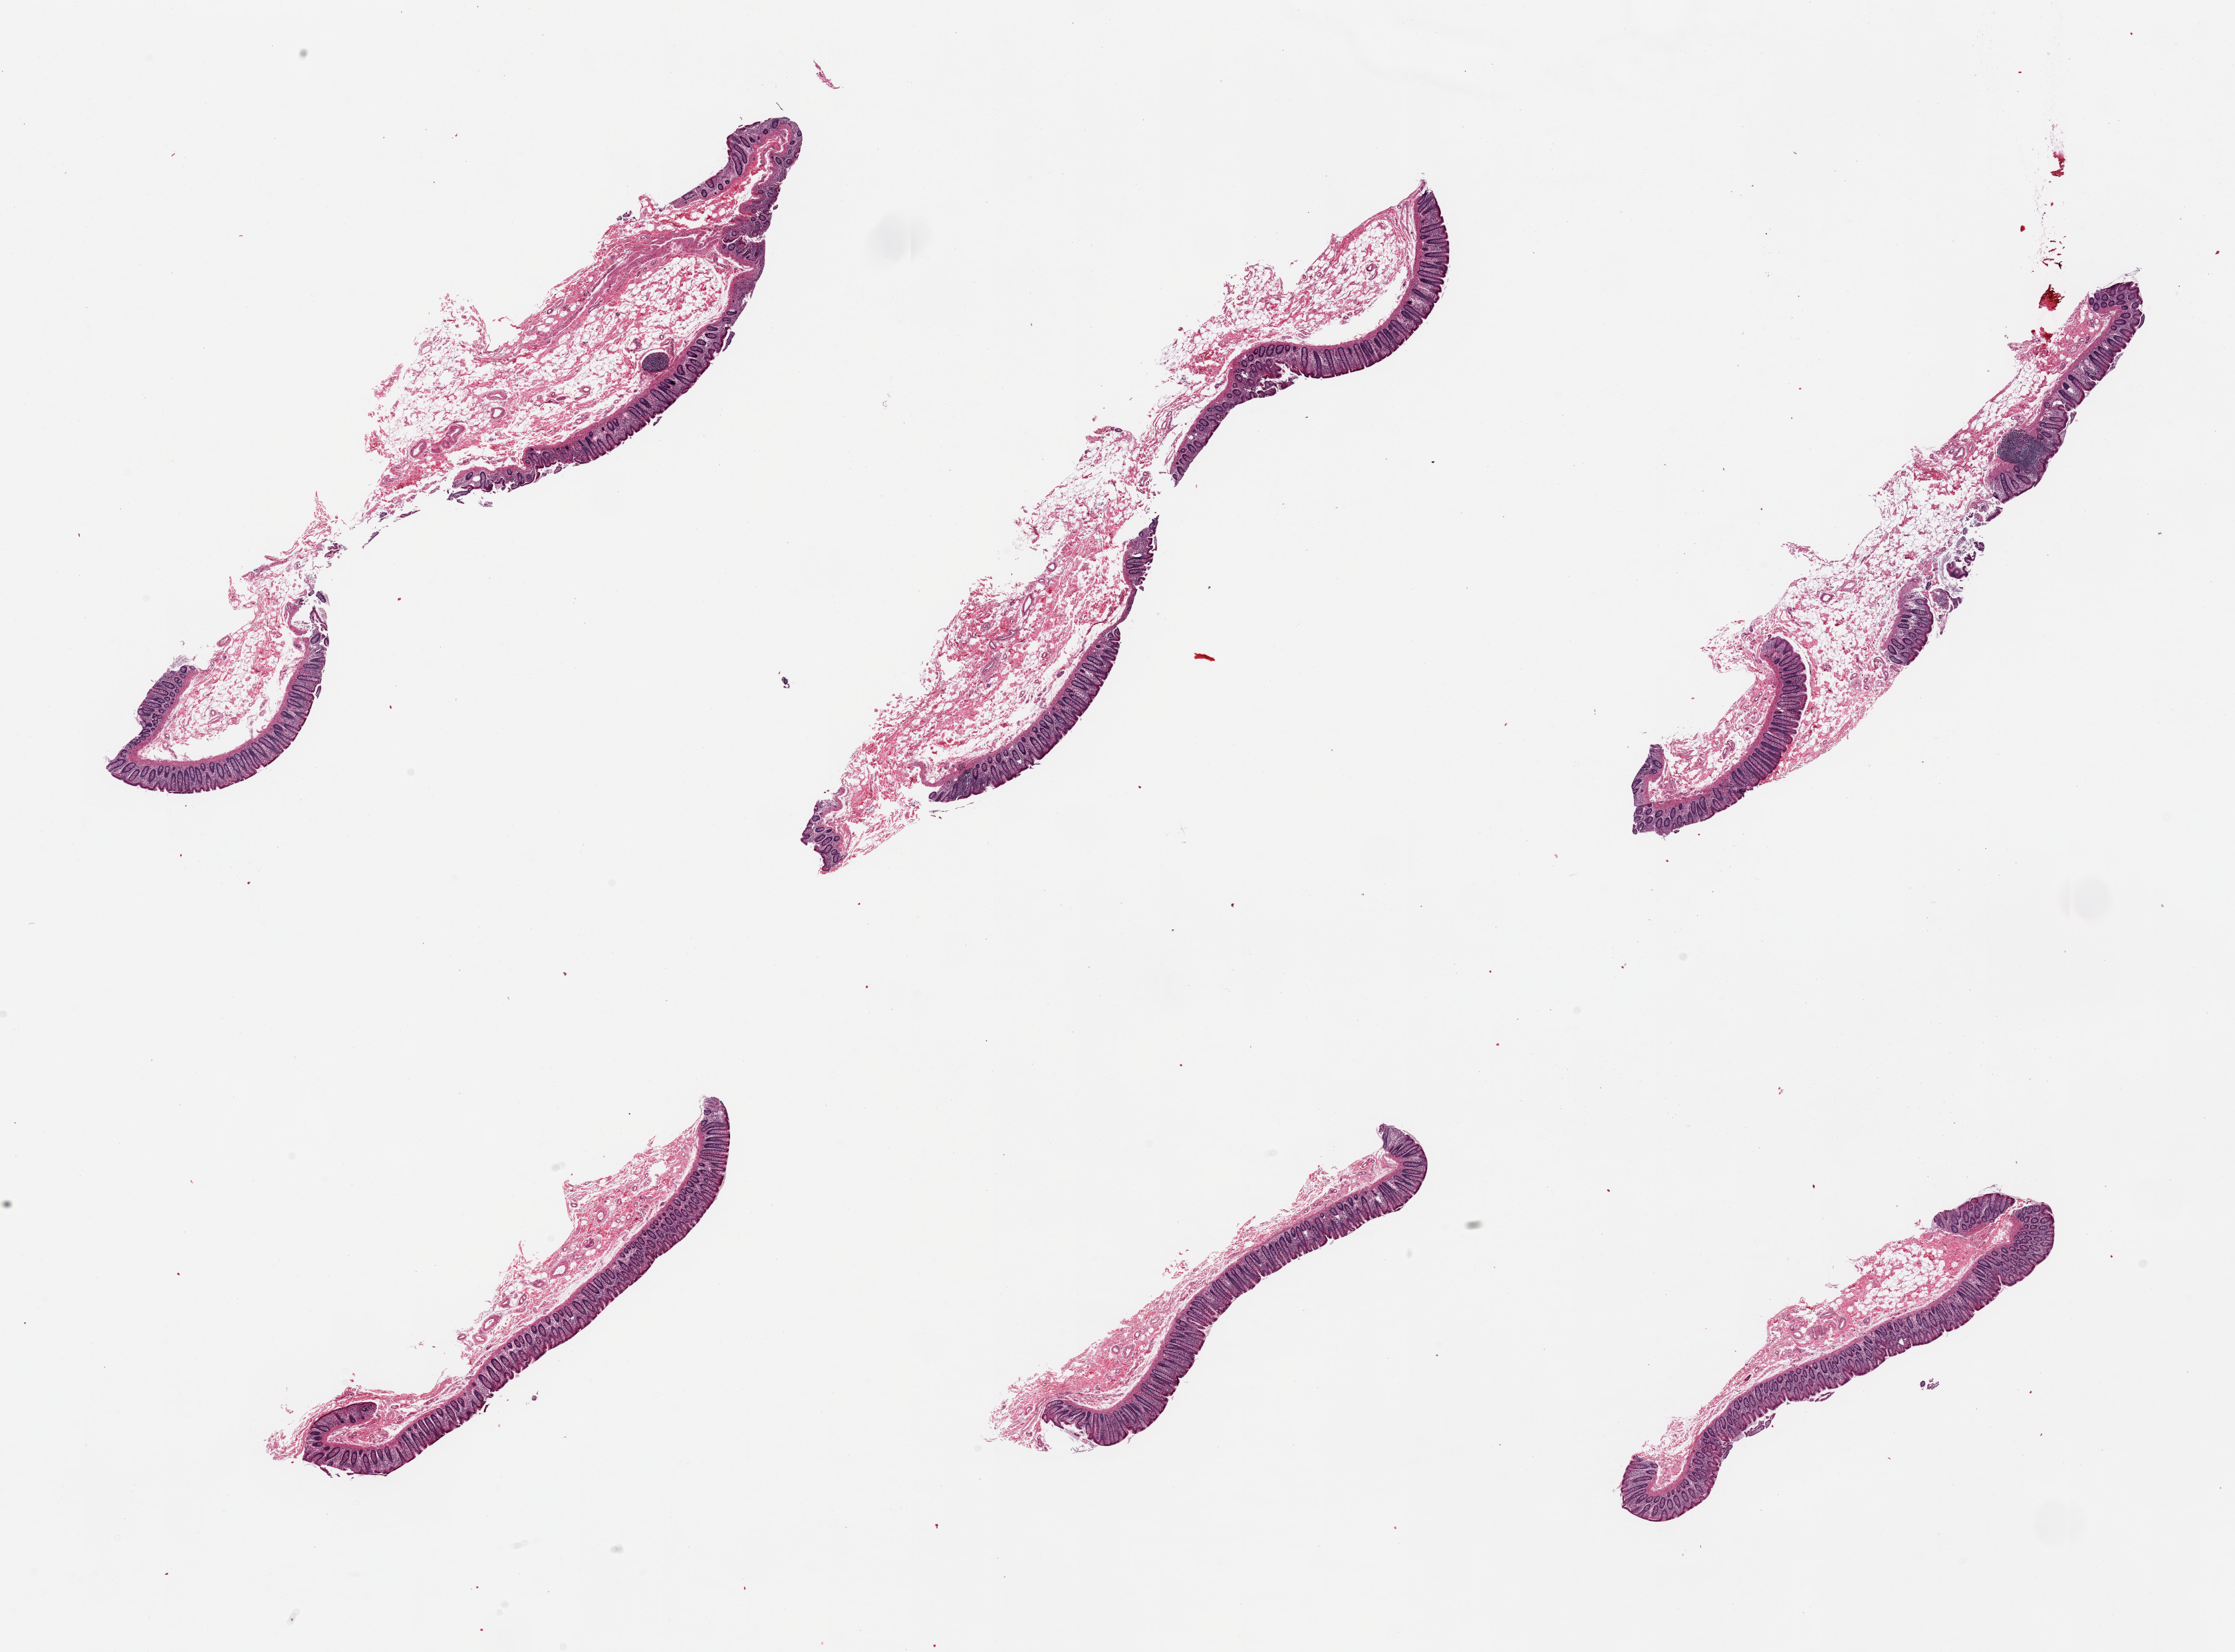
Whole-slide image, H&E stain, low-resolution overview of the scanned area, about 26.6 x 19.7 mm. PAXgene-fixed paraffin-embedded (PFPE) section. Sampled site (target tissue): ileum. Donor tissue sample. Female donor.
- review note (as recorded): 6 pieces, target lymphoid aggregates less than 5%